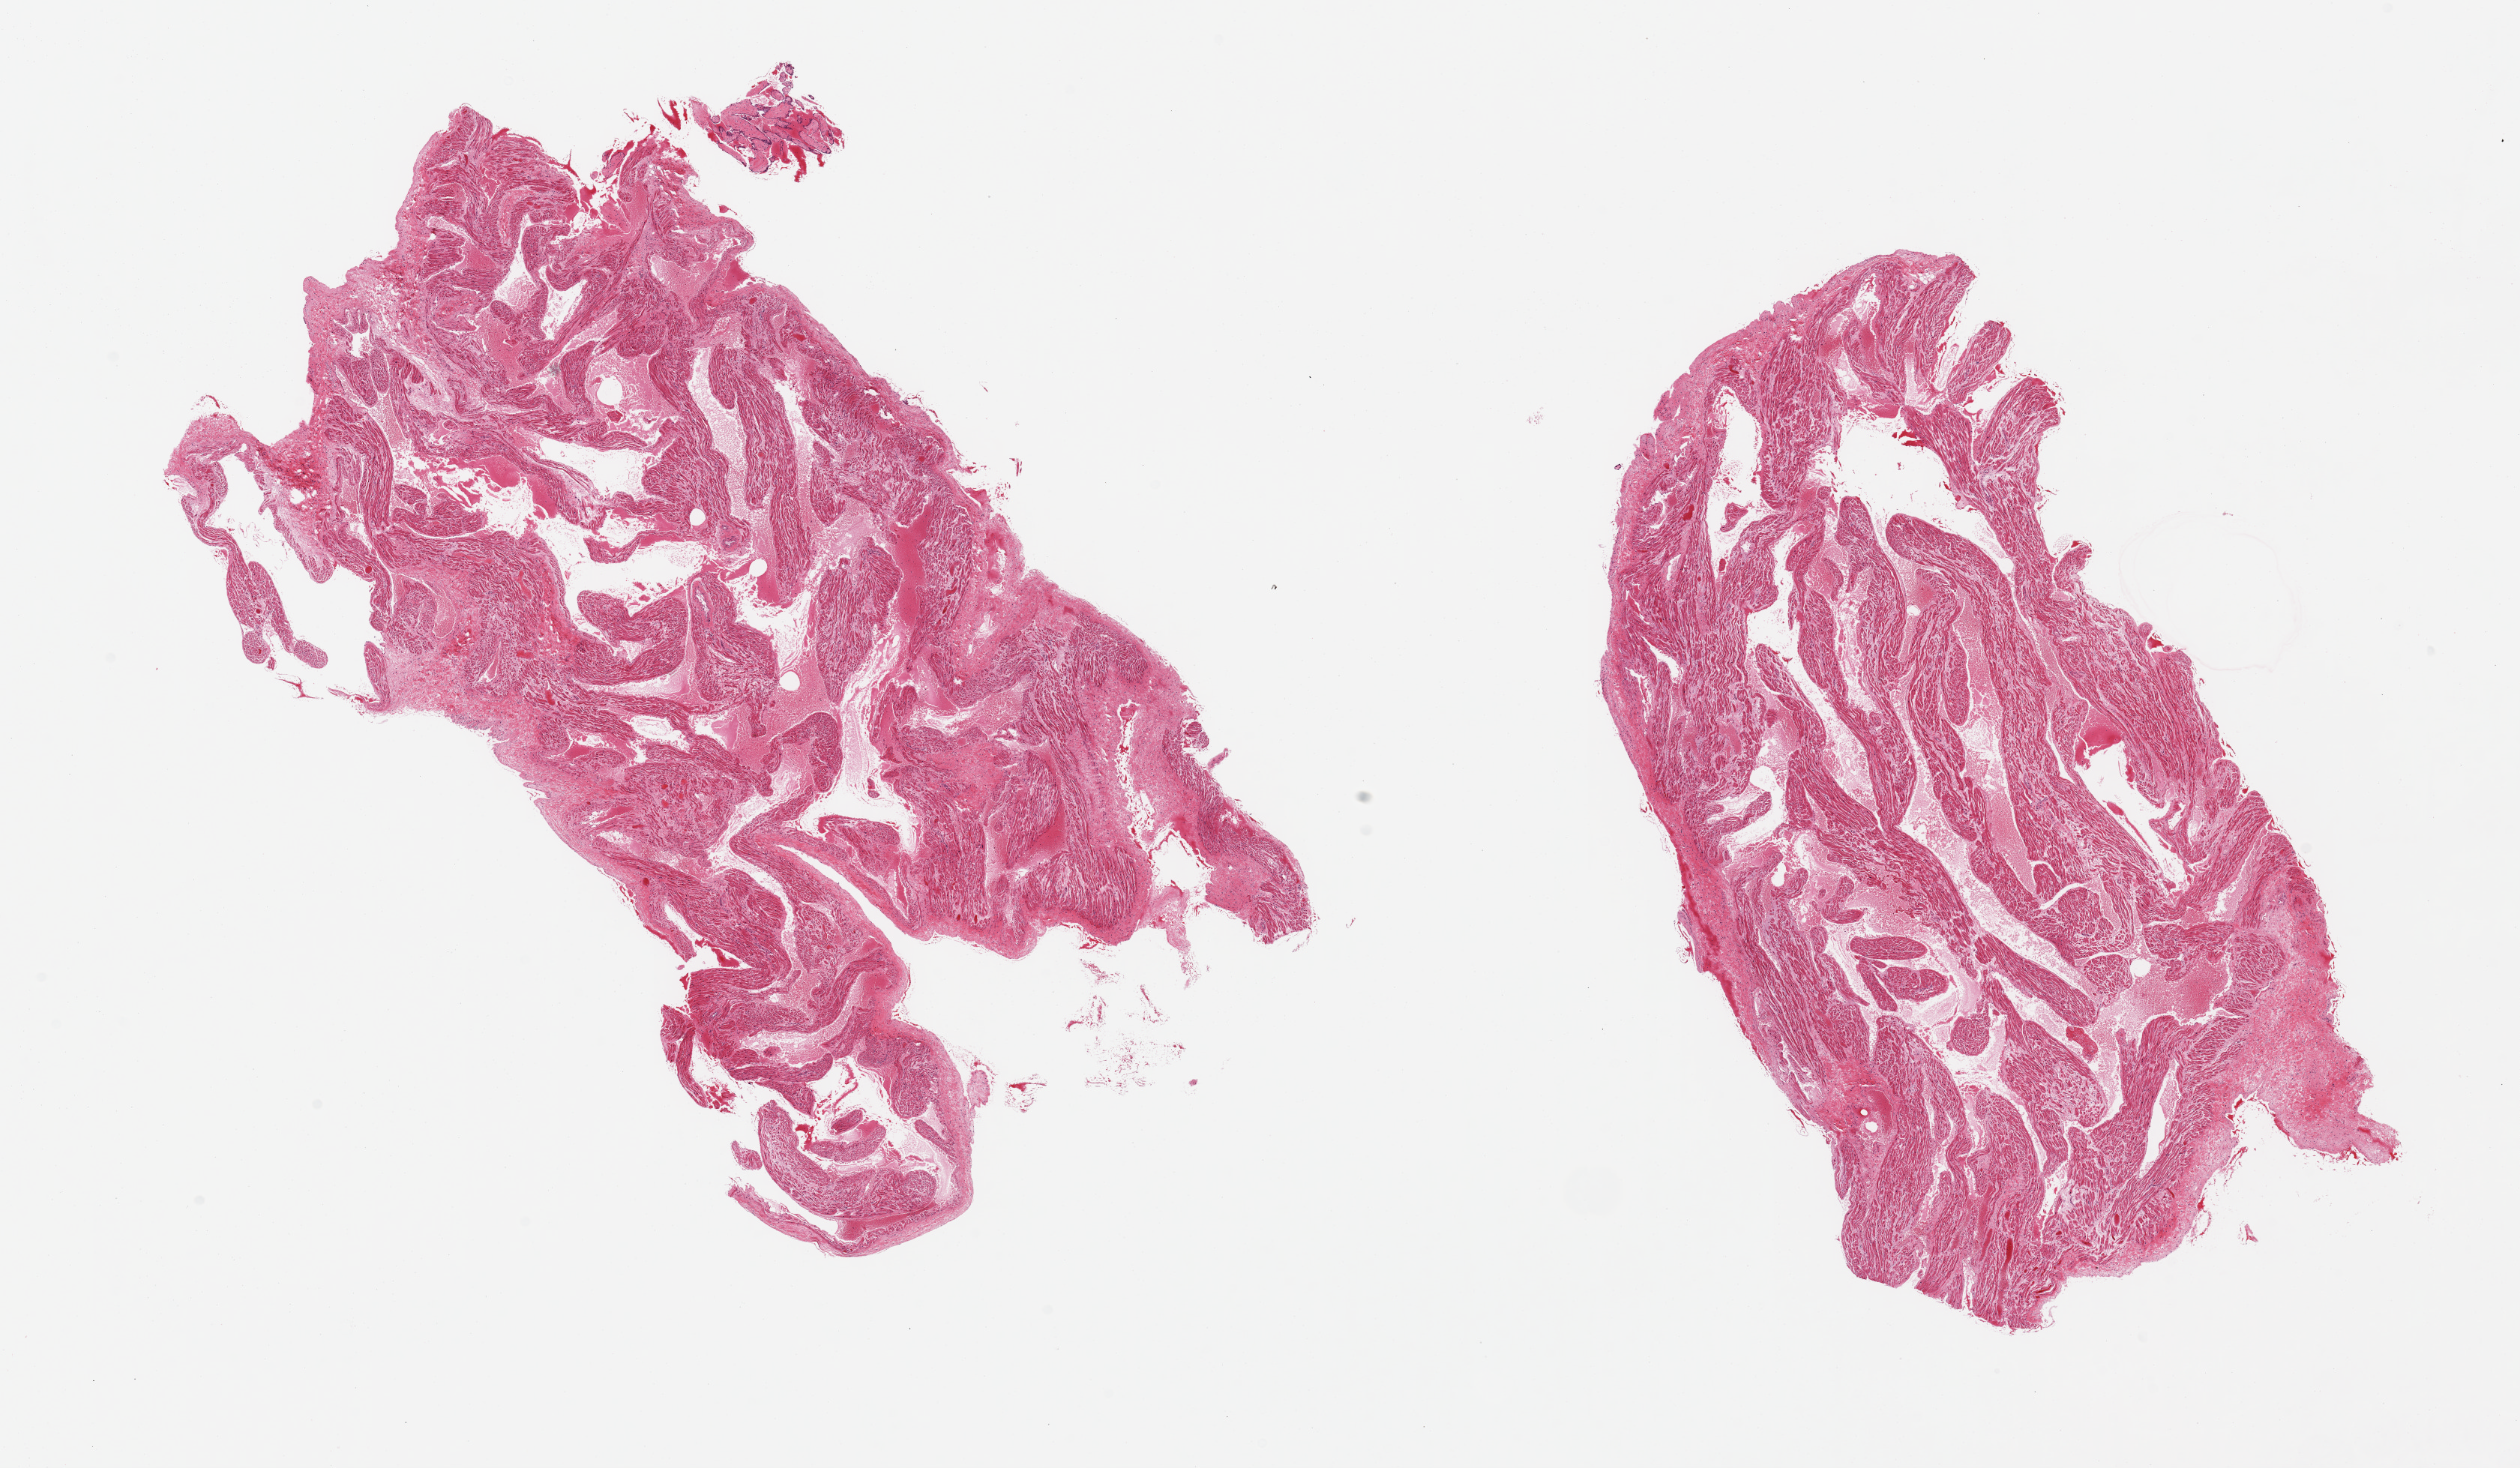
Whole-slide image, H&E stain, brightfield, low-resolution overview of the scanned area, about 26.6 x 15.5 mm (slide scanned at 20x); PAXgene-fixed paraffin-embedded (PFPE) section; target tissue: auricular appendage; donor tissue sample. Donor: female.
Pathologist's review note for this sample: 2 pieces.